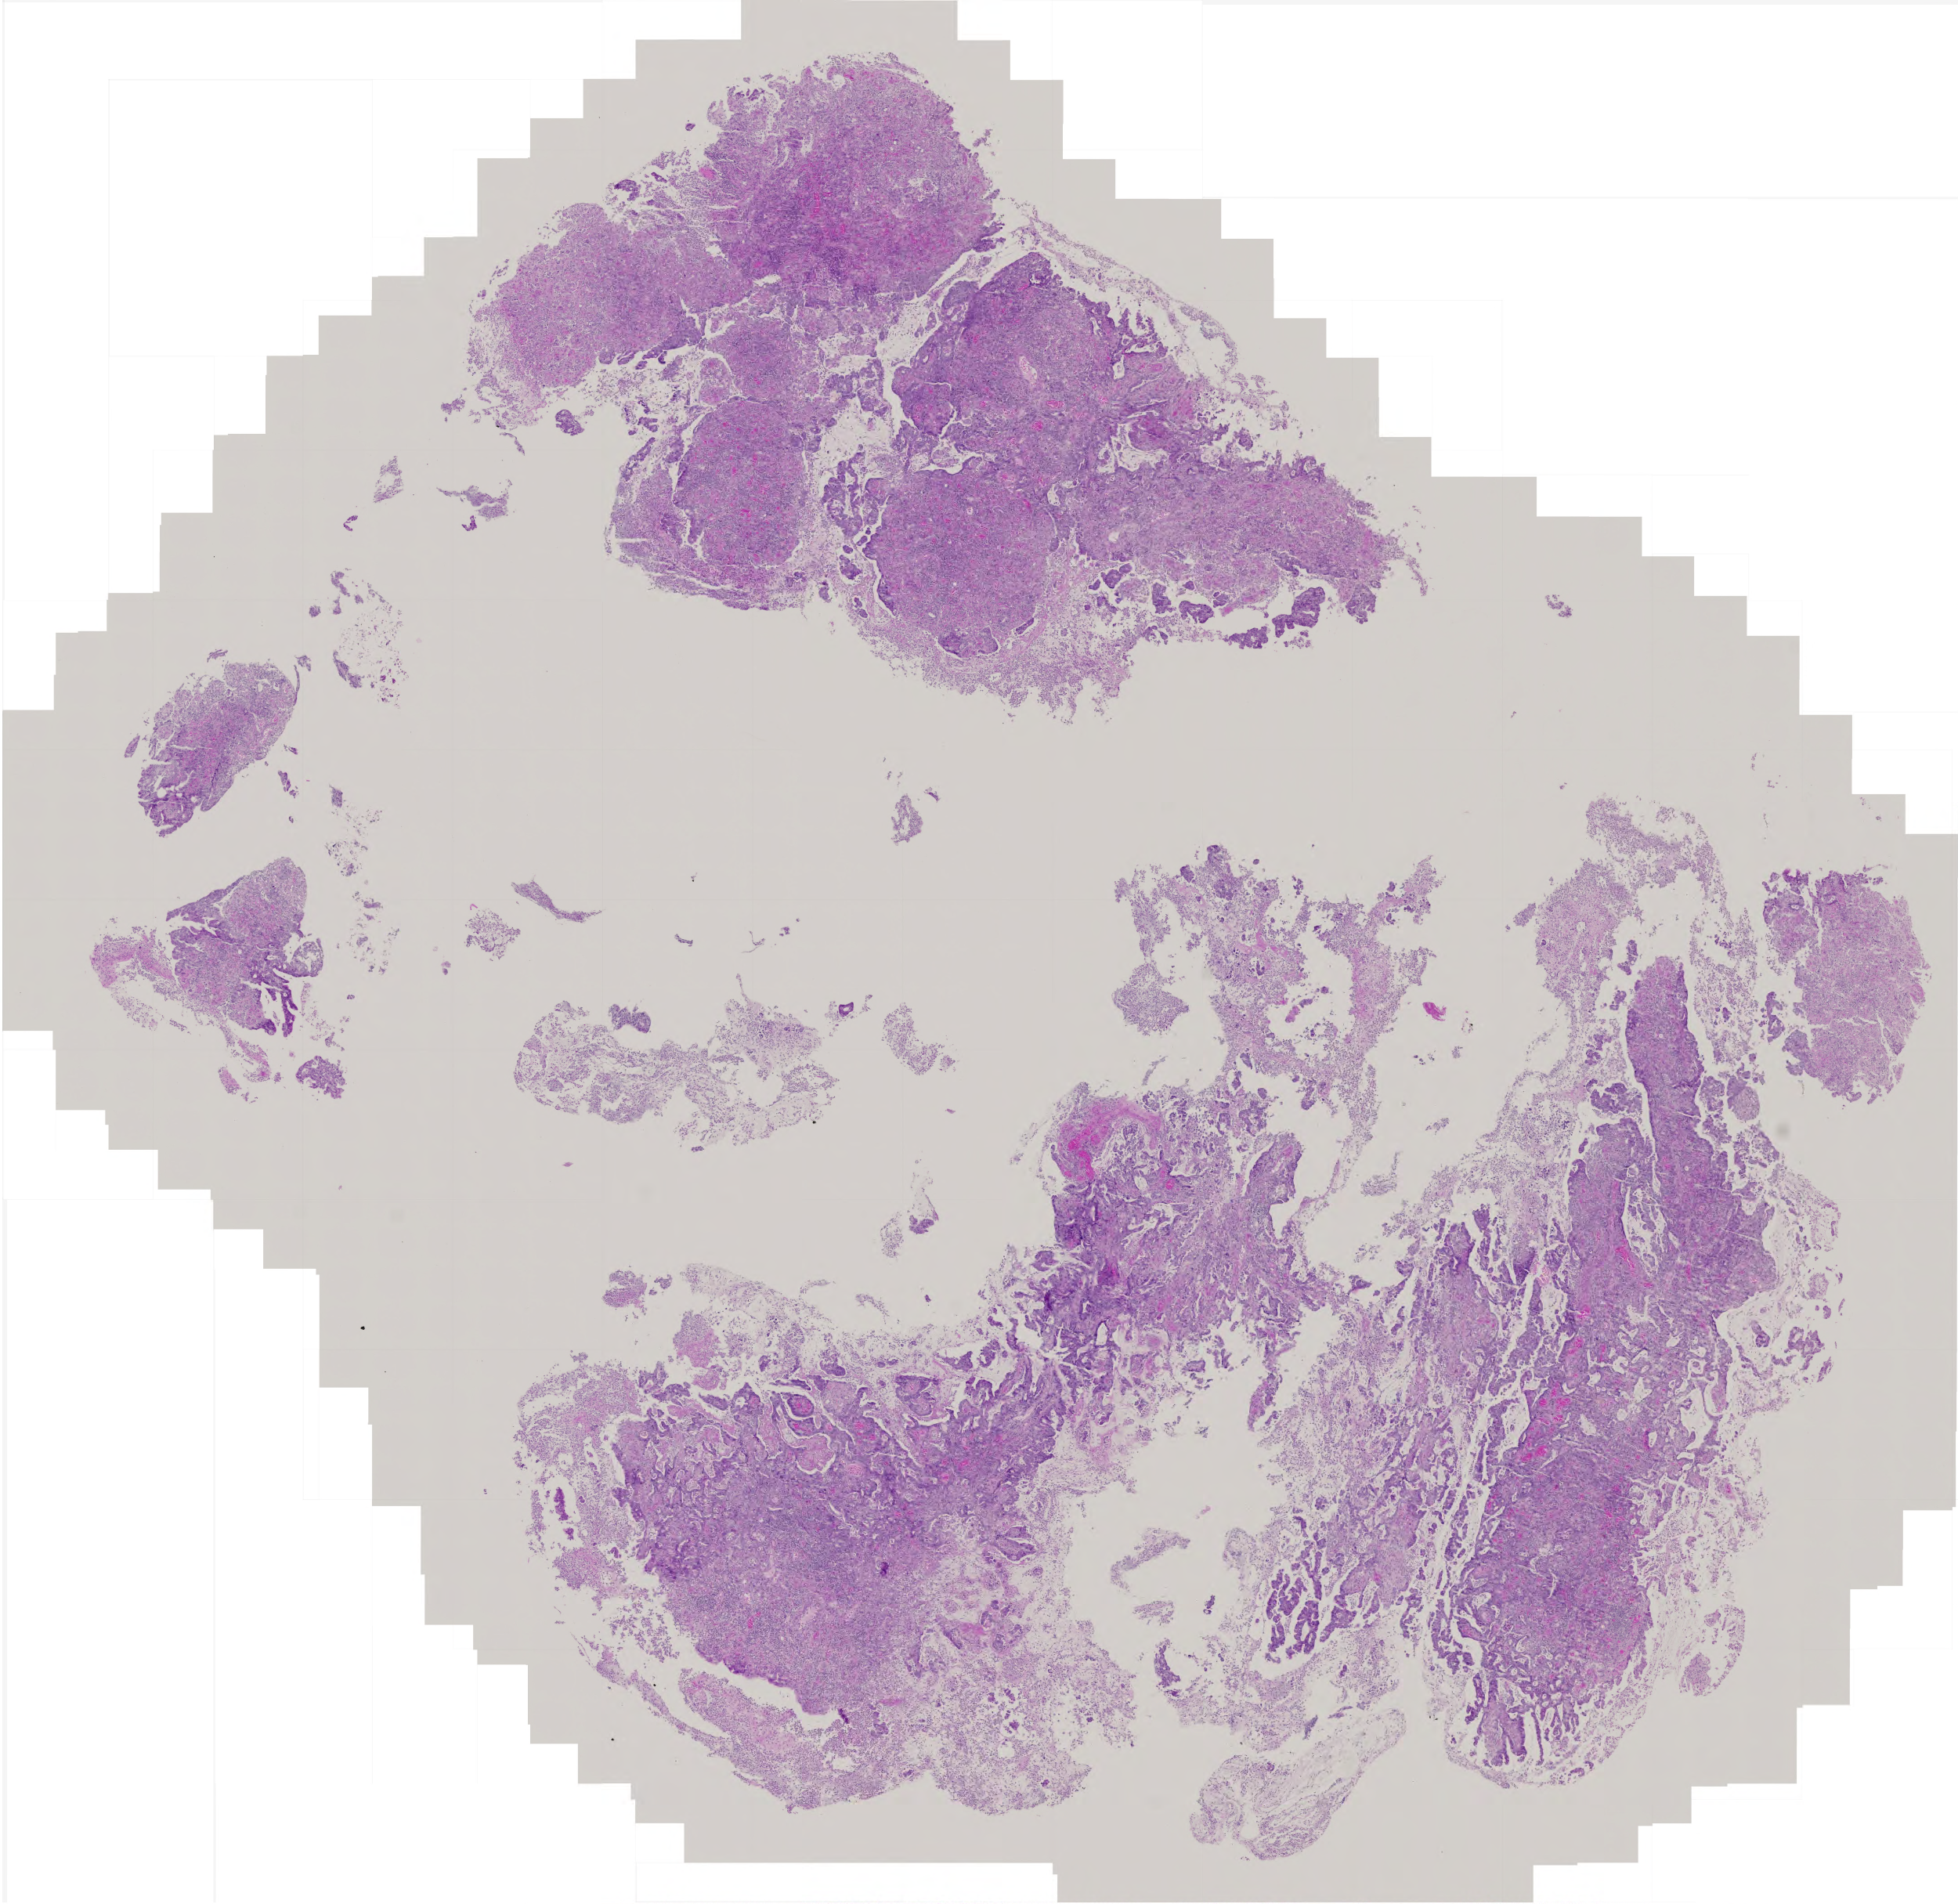
Digitized H&E tissue section (whole slide), whole scanned area (about 5.0 x 4.9 mm) shown as a low-resolution overview. Formalin-fixed paraffin-embedded (FFPE) diagnostic section. Stomach, primary tumour sample. Female patient; age at initial diagnosis 83 years. Histologic grade: G3 (poorly differentiated).
Diagnosis: Adenocarcinoma, intestinal type (gastric antrum). TNM: T2 N2 M0. Lymph nodes positive (case pathology): 7 of 32 examined. AJCC pathologic stage: IIIA (5th edition).